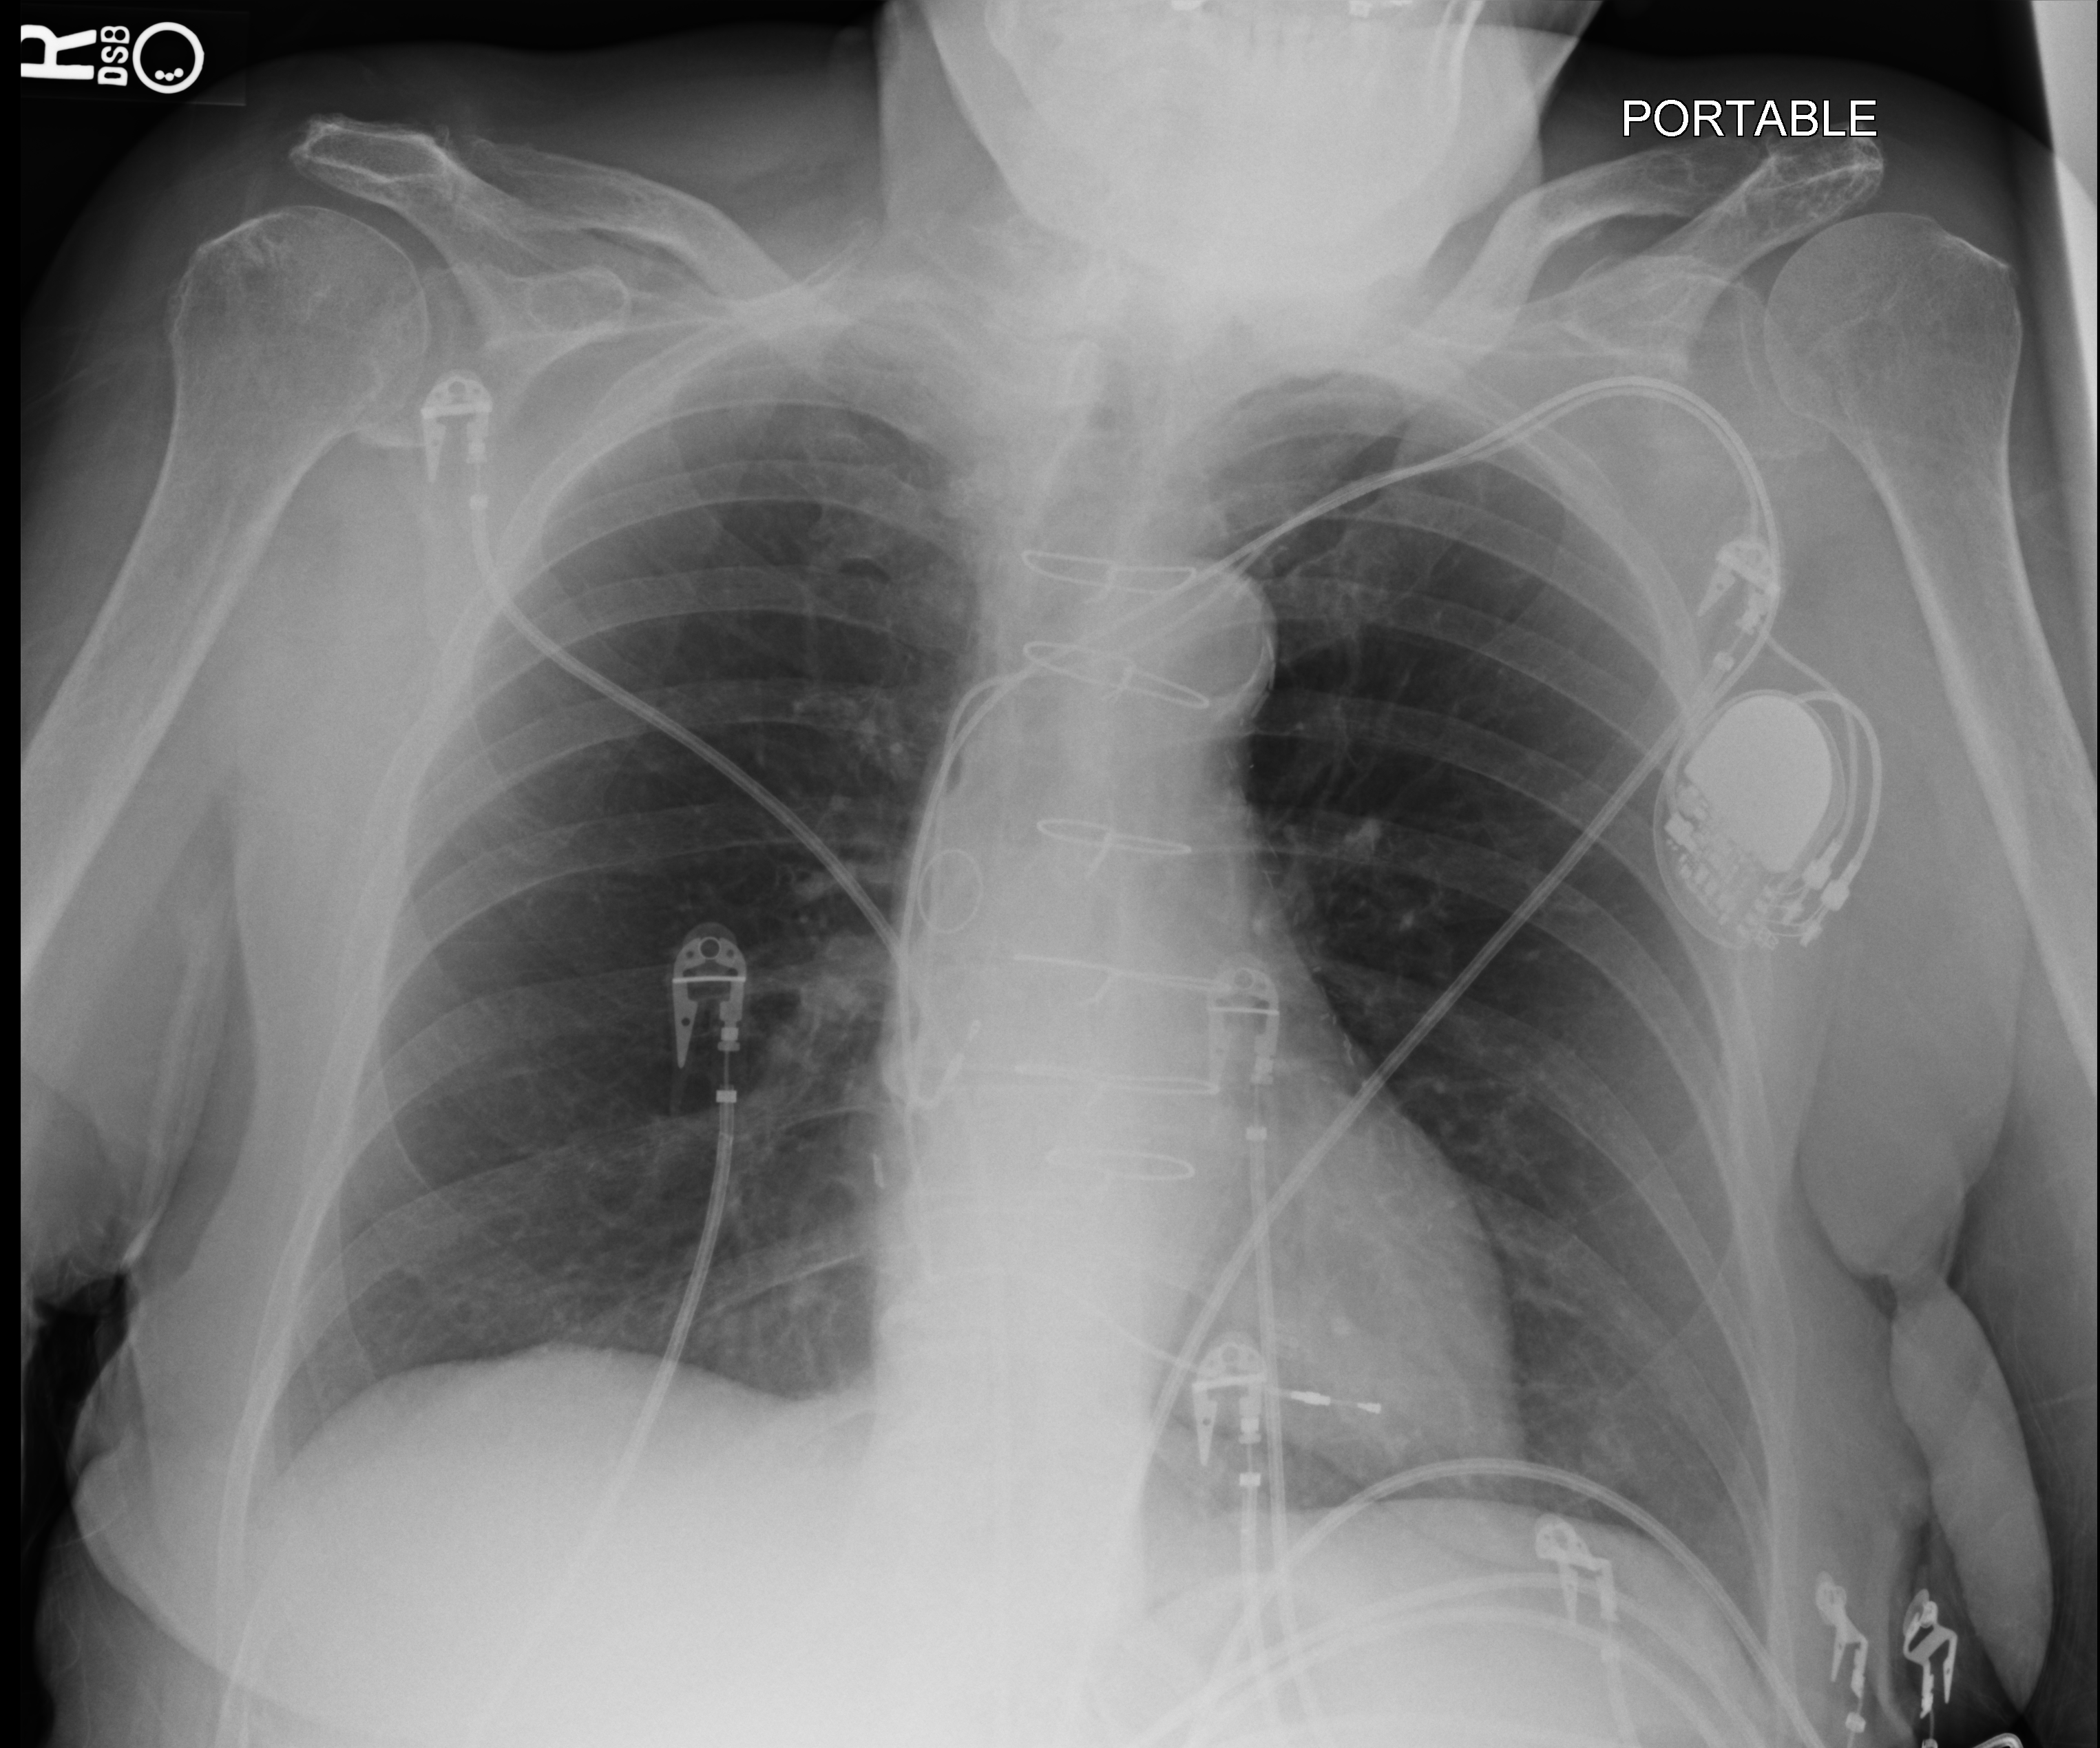
Bedside chest radiograph (computed radiography). Female patient hospitalised with COVID-19, age 75–90 years.
Hospital-stay facts (about this admission, not read from this image; timing relative to this image not recorded):
- length of hospital stay: 5 days
- admitted to intensive care during this hospital stay: no
- mechanically ventilated during this hospital stay: no